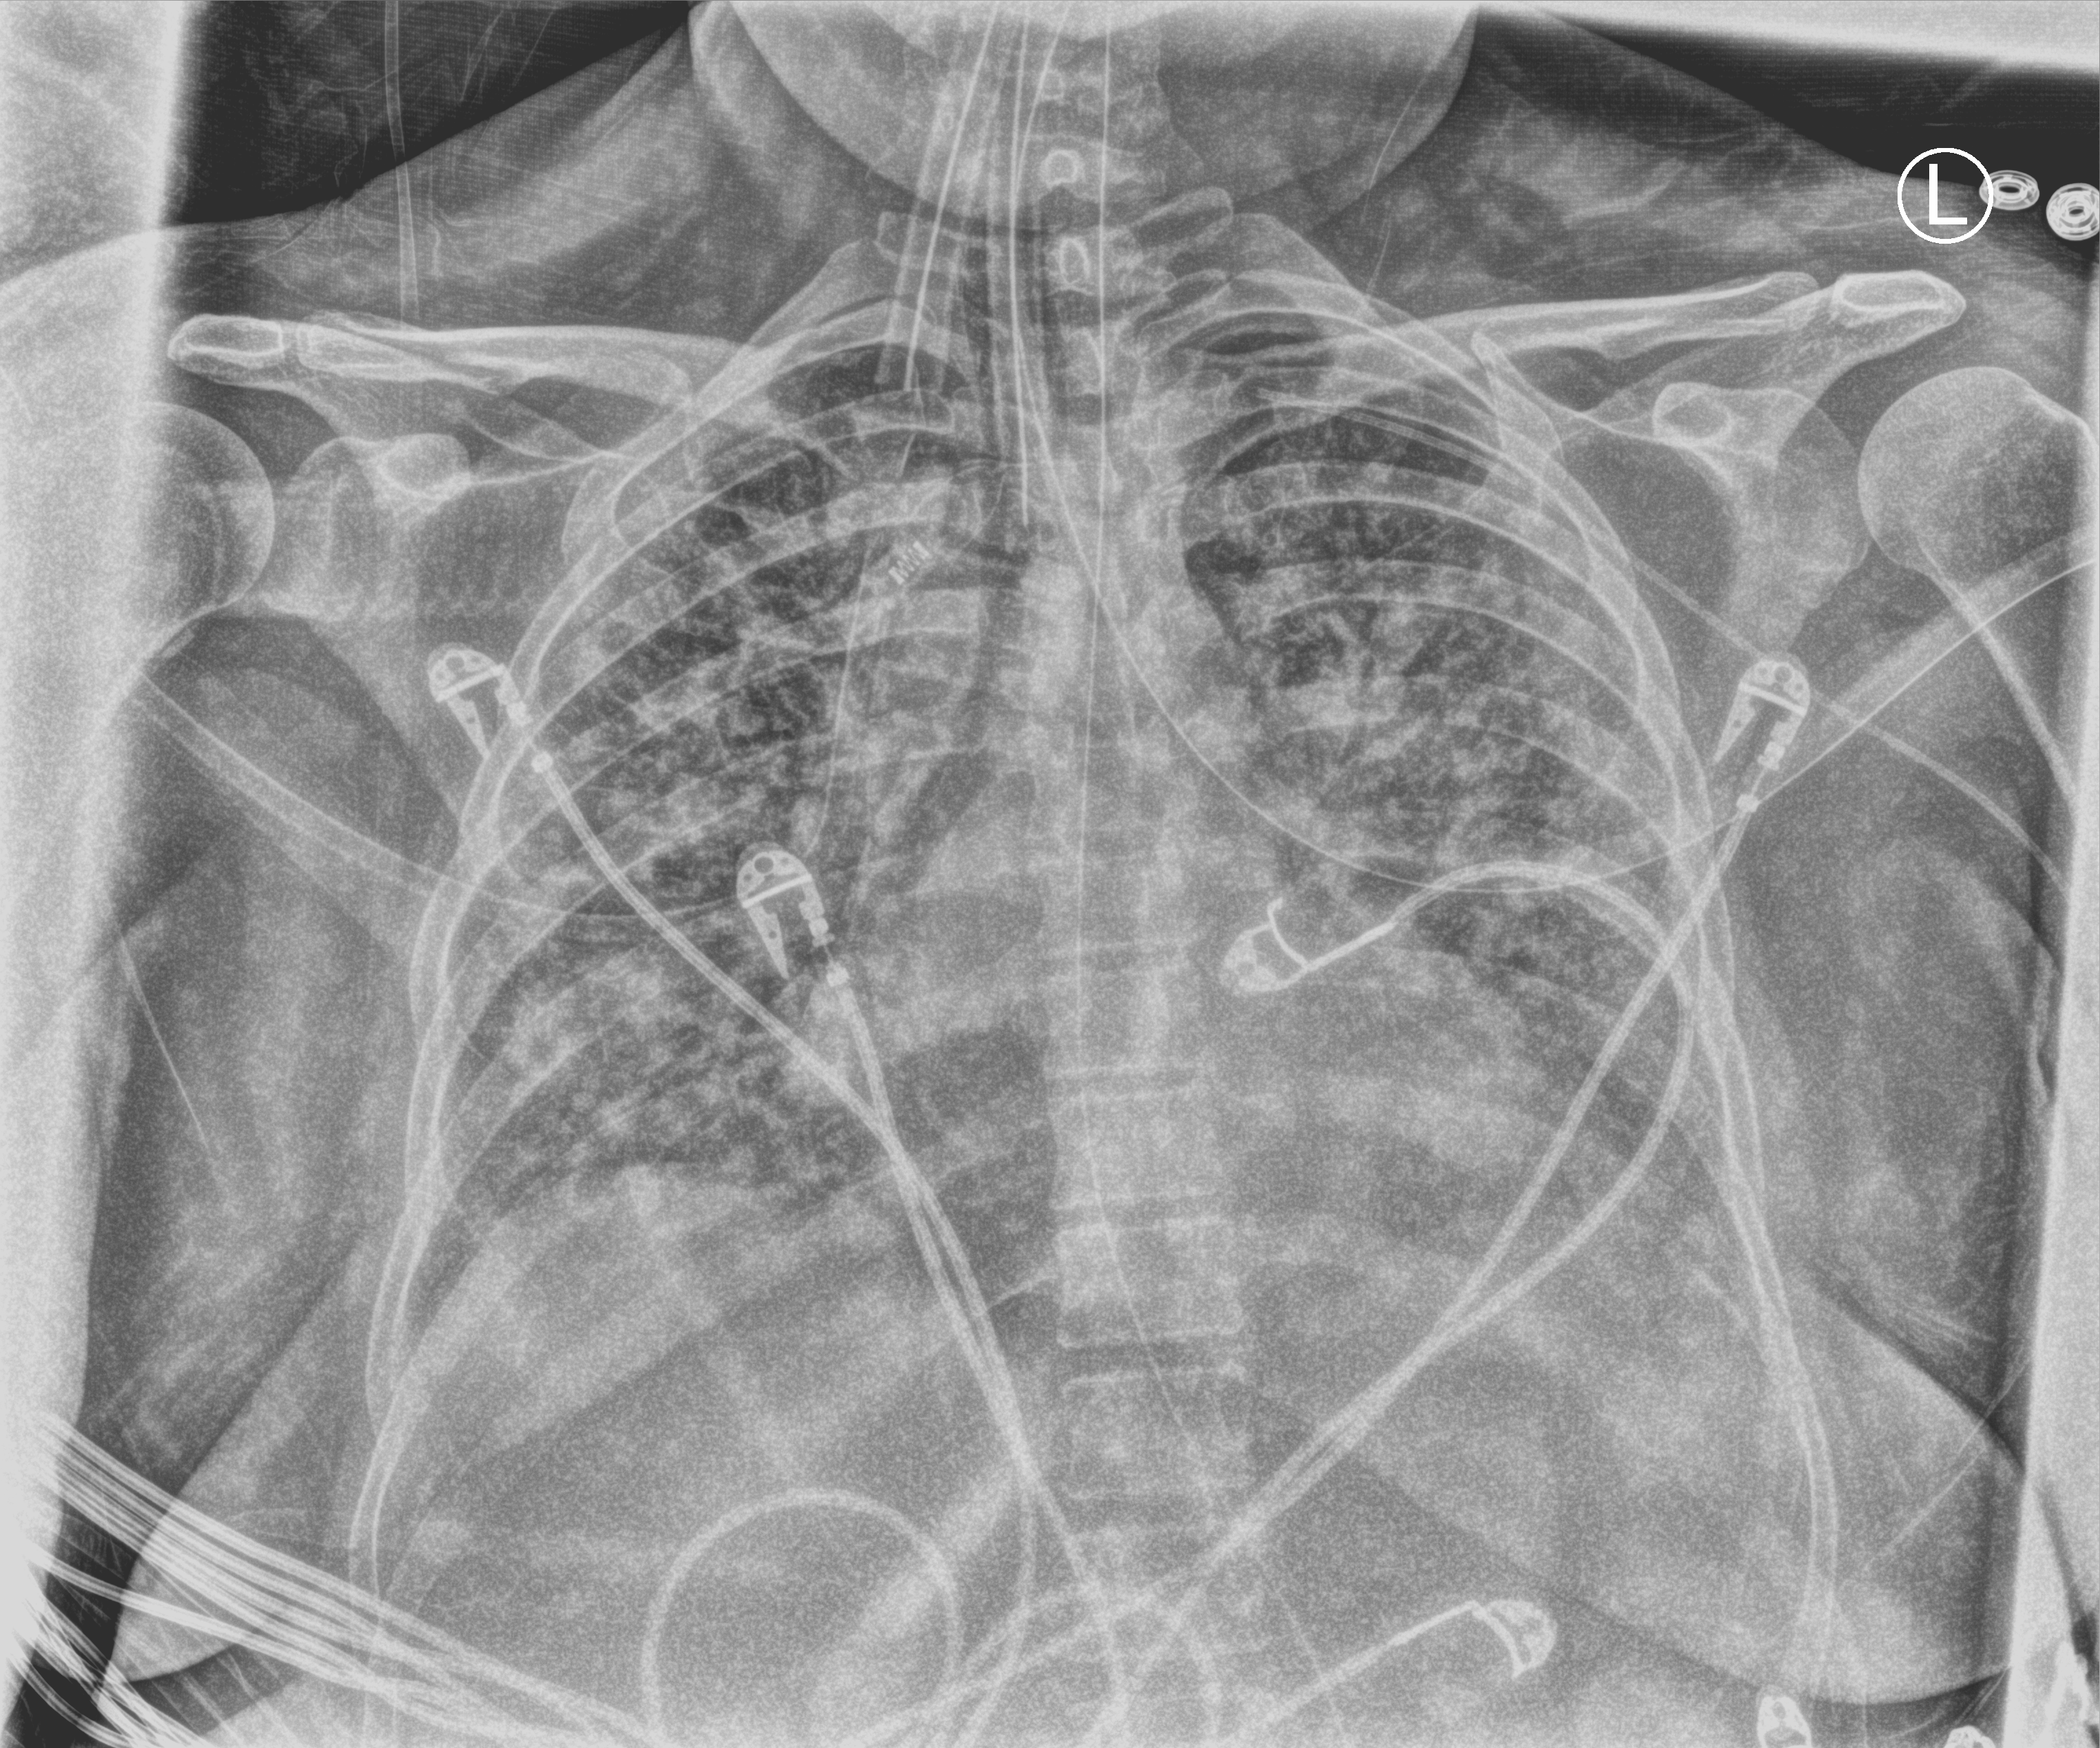
Chest X-ray (portable); anteroposterior (AP) projection. Patient hospitalised with COVID-19; female, aged 18–59 years.
Hospital-stay facts (about this admission, not read from this image; timing relative to this image not recorded):
- mechanically ventilated during this hospital stay: yes
- COPD (admission record): no